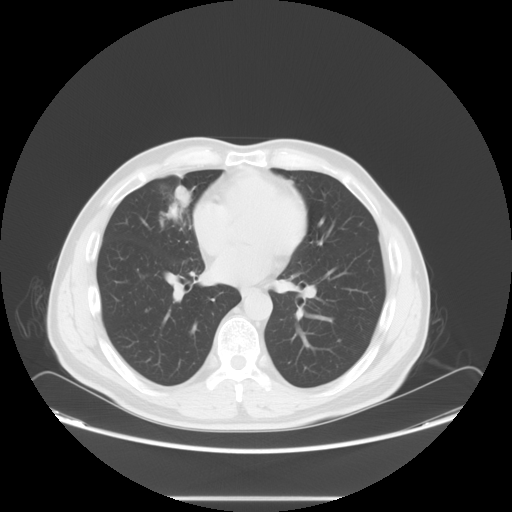
Chest CT, one axial slice. Slice 36 of 73 in the series (ordered by position). Reconstruction kernel STANDARD. 120 kVp. Lung window (W 1500 / L -600 HU). 512 × 512 image matrix, field of view 429 × 429 mm. Male patient, age 47 years. Case-level facts recorded for this patient, not image findings: clinical TNM (as recorded): T1c N3 M0.
Structures marked on this image (rectangle marked by the reading radiologist):
- lung tumour (recorded histology: adenocarcinoma): bounding box [x1, y1, x2, y2] px = [156, 180, 195, 223]